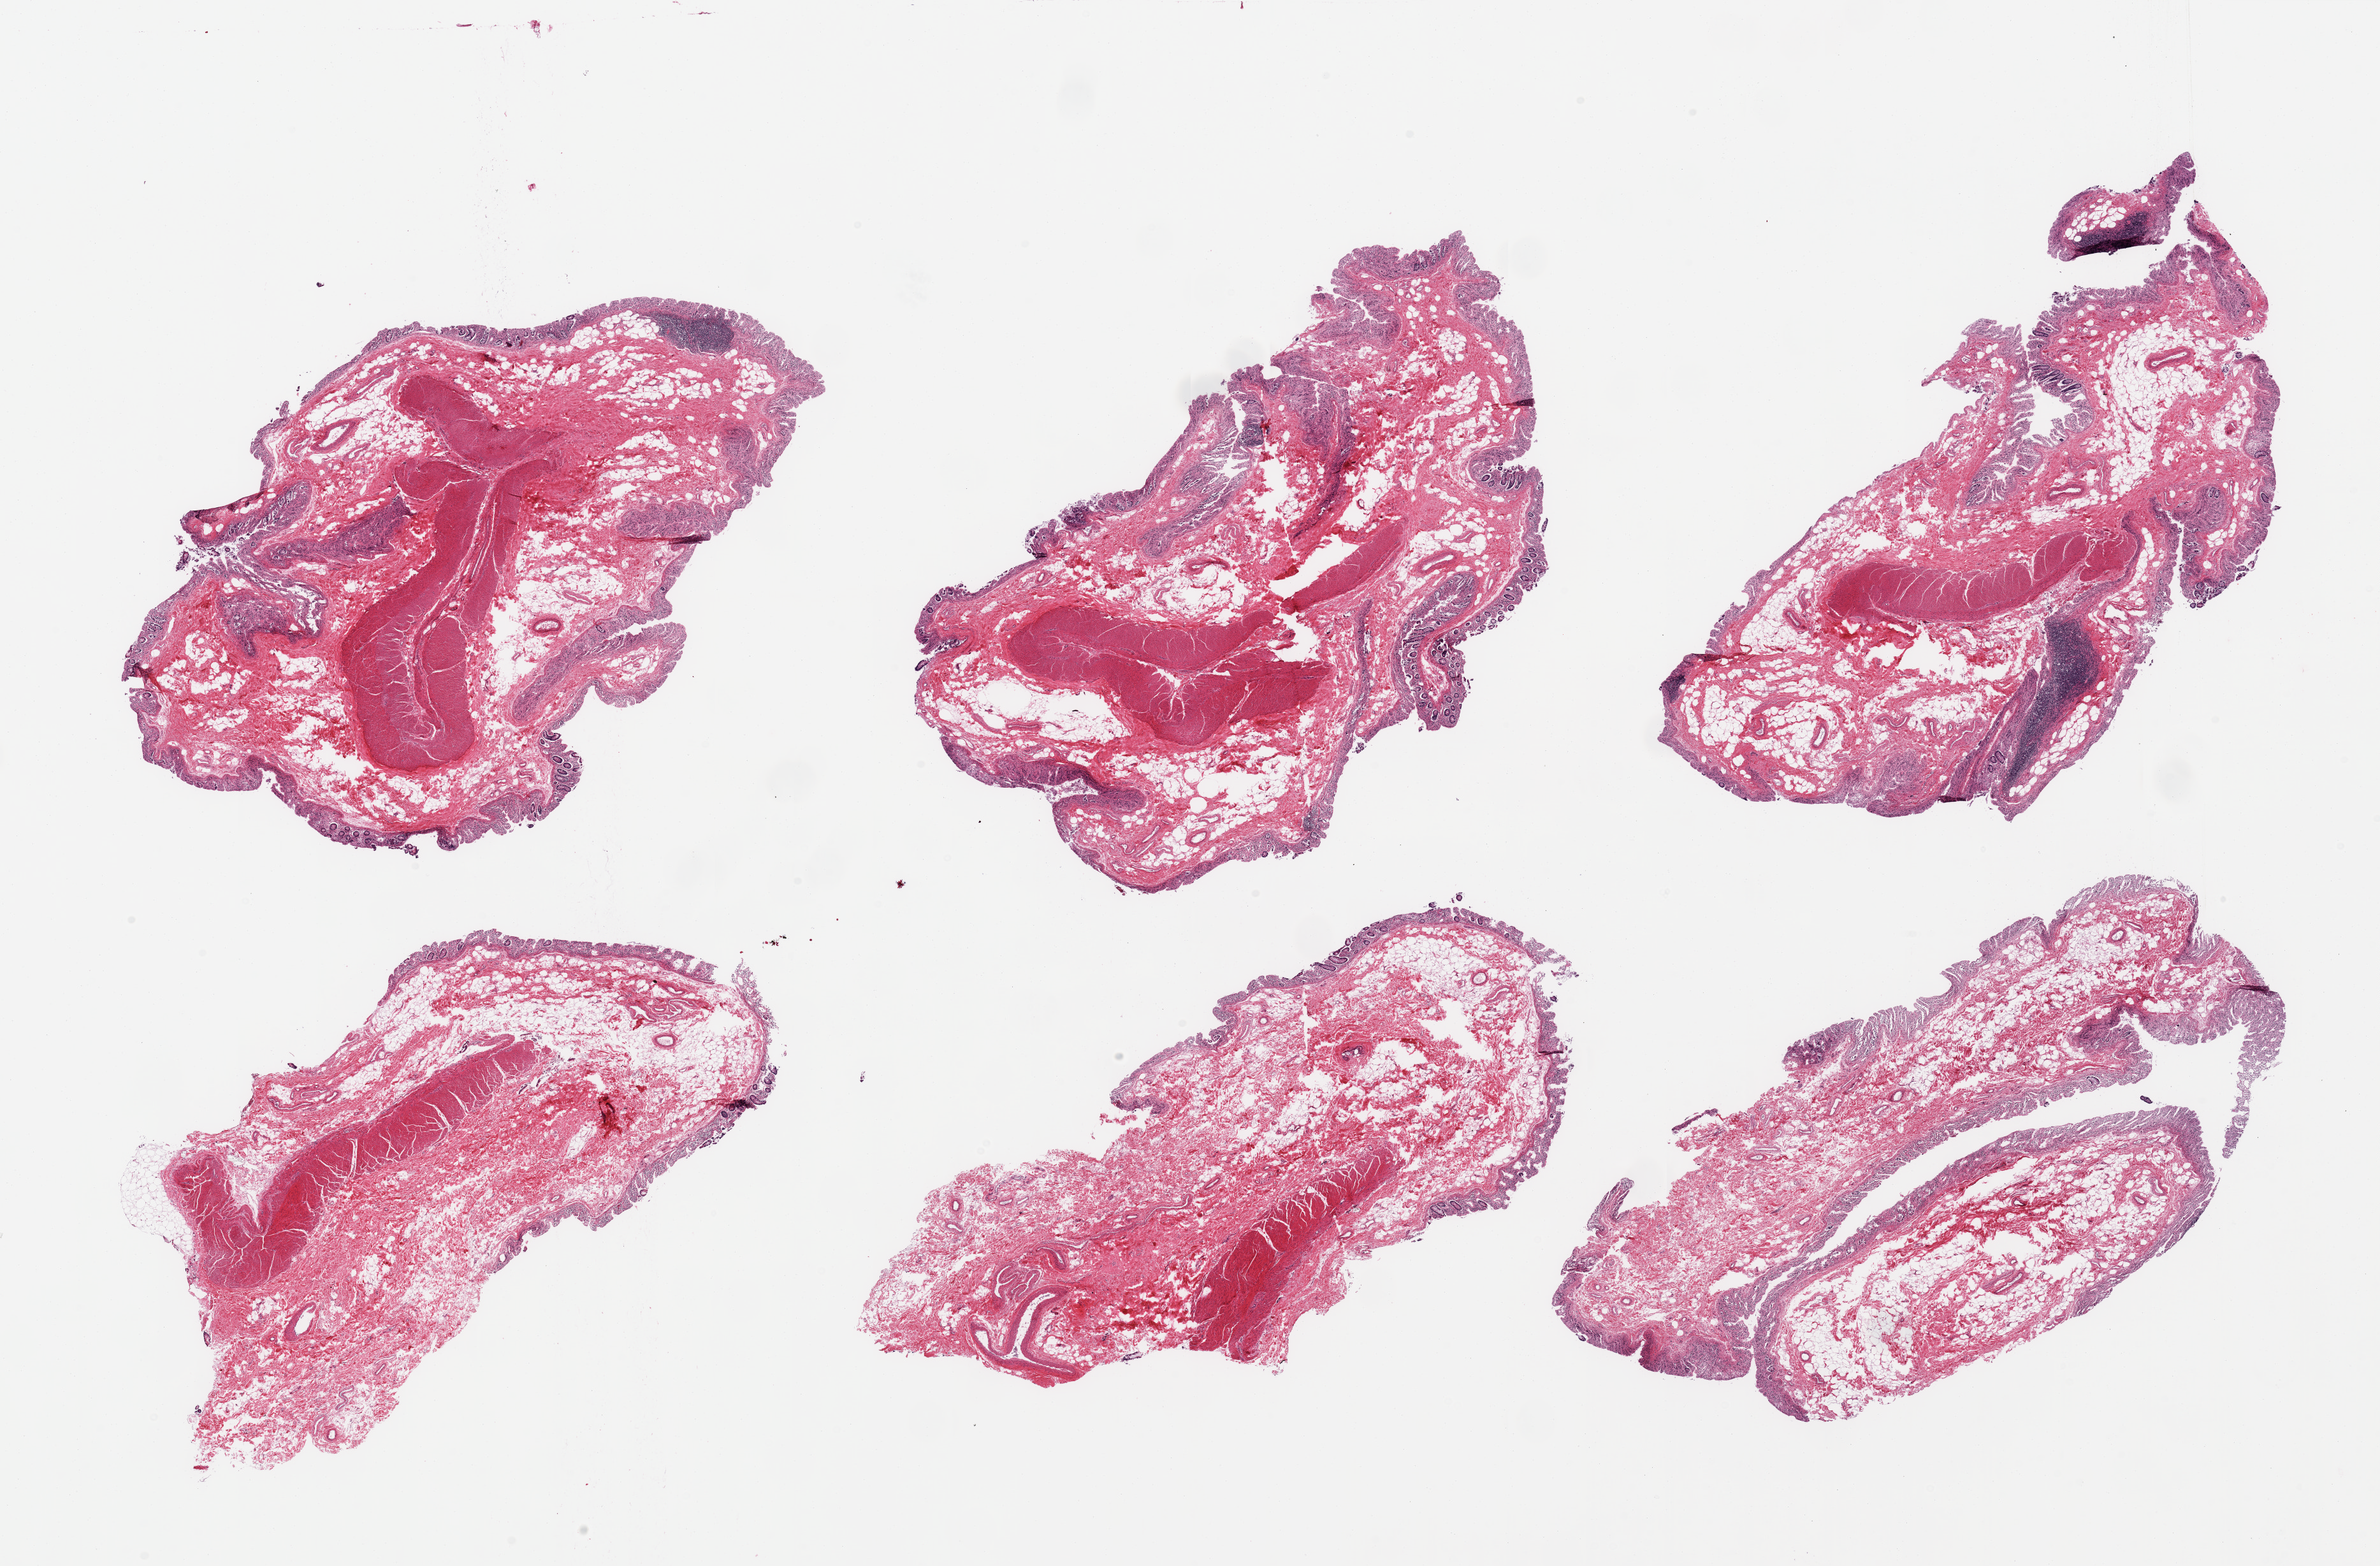
Digitized H&E-stained section, whole scanned area (about 29.5 x 19.4 mm, acquisition: 20x scan) shown as a low-resolution overview. PAXgene-fixed paraffin-embedded (PFPE) section. Section of ileum (target tissue). Donor tissue sample. Donor sex: male.
* pathologist's review note for this sample: 6 pieces; colon/cecum, not ileum